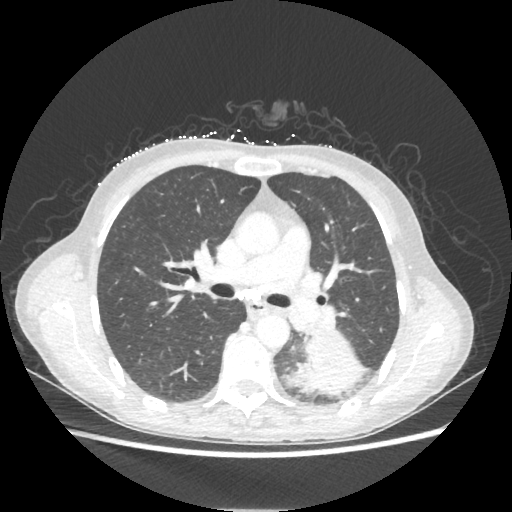
Chest CT, one axial slice. Slice 132 of 221 in the series (ordered by position). 80 kVp. Lung window (W 1500 / L -600 HU). 1.25 mm slice thickness. 512 × 512 image matrix. Patient: female, 53 years. From the clinical record (not read from this slice): clinical TNM (as recorded): T3 N0 M0.
Outlined on this slice (rectangle marked by the reading radiologist):
- lung tumour (recorded histology: adenocarcinoma): bounding box (x1, y1, x2, y2) in pixels: (293, 332, 366, 397)